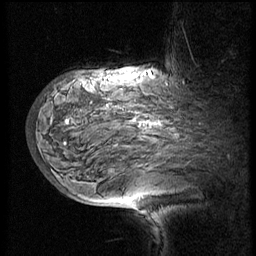
Breast MRI (dynamic contrast-enhanced), one sagittal slice. Position 43 of 60 along the scan axis. 3 images stored at this slice position (order not interpretable as contrast timing). 1.5 T. TE 4.2 ms, TR 8.9 ms. 2.5 mm slice thickness. 256 × 256 image matrix, field of view 200 × 200 mm. Female patient, age 57 years. From the clinical record (not read from this slice): setting: breast cancer imaged before/during neoadjuvant chemotherapy; receptor status: HER2-positive.
Outlined on this slice (semi-automatically segmented with operator editing):
- analysis volume of interest (the breast-tissue region the enhancement analysis was run in; not a lesion): bounding box [x1, y1, x2, y2] px = [34, 75, 214, 171]
- tumour enhancement mask (voxels above the 140 % enhancement threshold inside the analysis volume of interest): [149, 120, 161, 124]